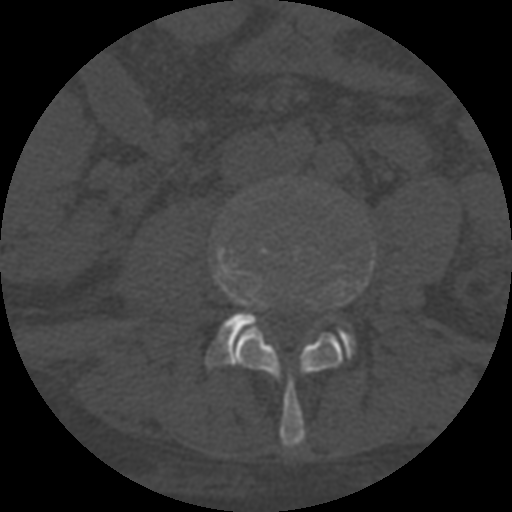
CT including the spine, one axial slice; position 222 of 708 along the scan axis; reconstruction kernel STANDARD; 120 kVp; one of 3 acquisitions stored at this slice position; bone window (W 1800 / L 400 HU); 1.25 mm slice thickness; 512 × 512 image matrix. Patient age 55 years. From the clinical record (not read from this slice): primary cancer: colon; vertebrae with lytic lesions (as recorded): T12, L1, L5.
Outlined on this slice (semi-automatic segmentation, software-assisted and operator-edited):
- L3 vertebra: bounding box [x1, y1, x2, y2] px = [233, 327, 343, 447]
- L4 vertebra: [206, 248, 373, 367]